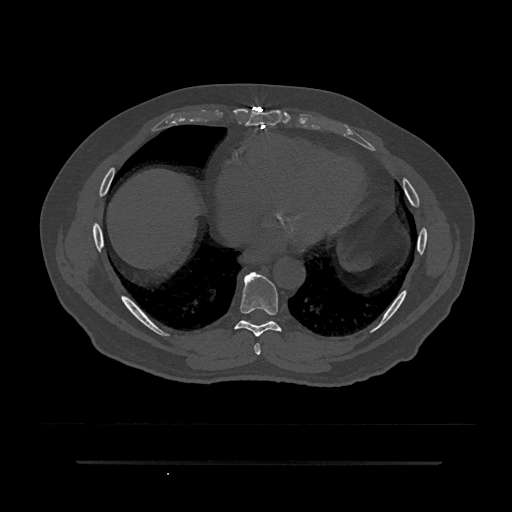
CT including the spine, one axial slice. Slice 425 of 797 in the series (ordered by position). Reconstruction kernel Br40s/3. Bone window (W 1800 / L 400 HU). 0.5 mm slice thickness. 512 × 512 image matrix, field of view 464 × 464 mm. Patient: male, 59 years. Case-level facts recorded for this patient, not image findings: primary cancer: bile ducts.
Outlined on this slice (semi-automatic segmentation, software-assisted and operator-edited):
- T7 vertebra: box from (x=254, y=343) to (x=261, y=355) px
- T8 vertebra: (x=234, y=272)–(x=282, y=337)